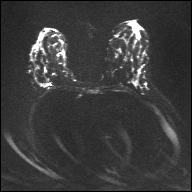
Breast MRI, one axial slice; slice 16 of 32 in the series (ordered by position); diffusion-weighted series; image 2 of 4 stored at this slice position (different b-values; order by instance number); 1.5 T; 4 mm slice thickness; 192 × 192 image matrix, field of view 360 × 360 mm. Female patient.
Outlined on this slice (expert manual segmentation):
- tumour on diffusion-weighted imaging: bounding box (x1, y1, x2, y2) in pixels: (43, 84, 49, 86)